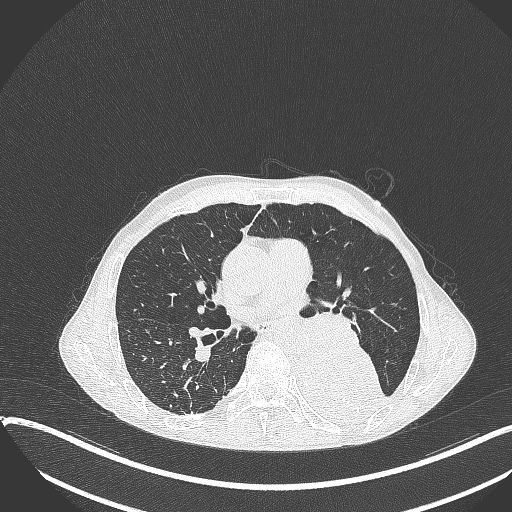
Chest CT, one axial slice; position 199 of 401 along the scan axis; 120 kVp; lung window (W 1500 / L -600 HU); 1 mm slice thickness; 512 × 512 image matrix, field of view 400 × 400 mm. Male patient, age 57 years. From the clinical record (not read from this slice): clinical TNM (as recorded): T4 N0 M0.
Annotated regions visible in this slice (rectangle marked by the reading radiologist):
- lung tumour (recorded histology: squamous cell carcinoma): bounding box (x1, y1, x2, y2) in pixels: (288, 332, 391, 426)